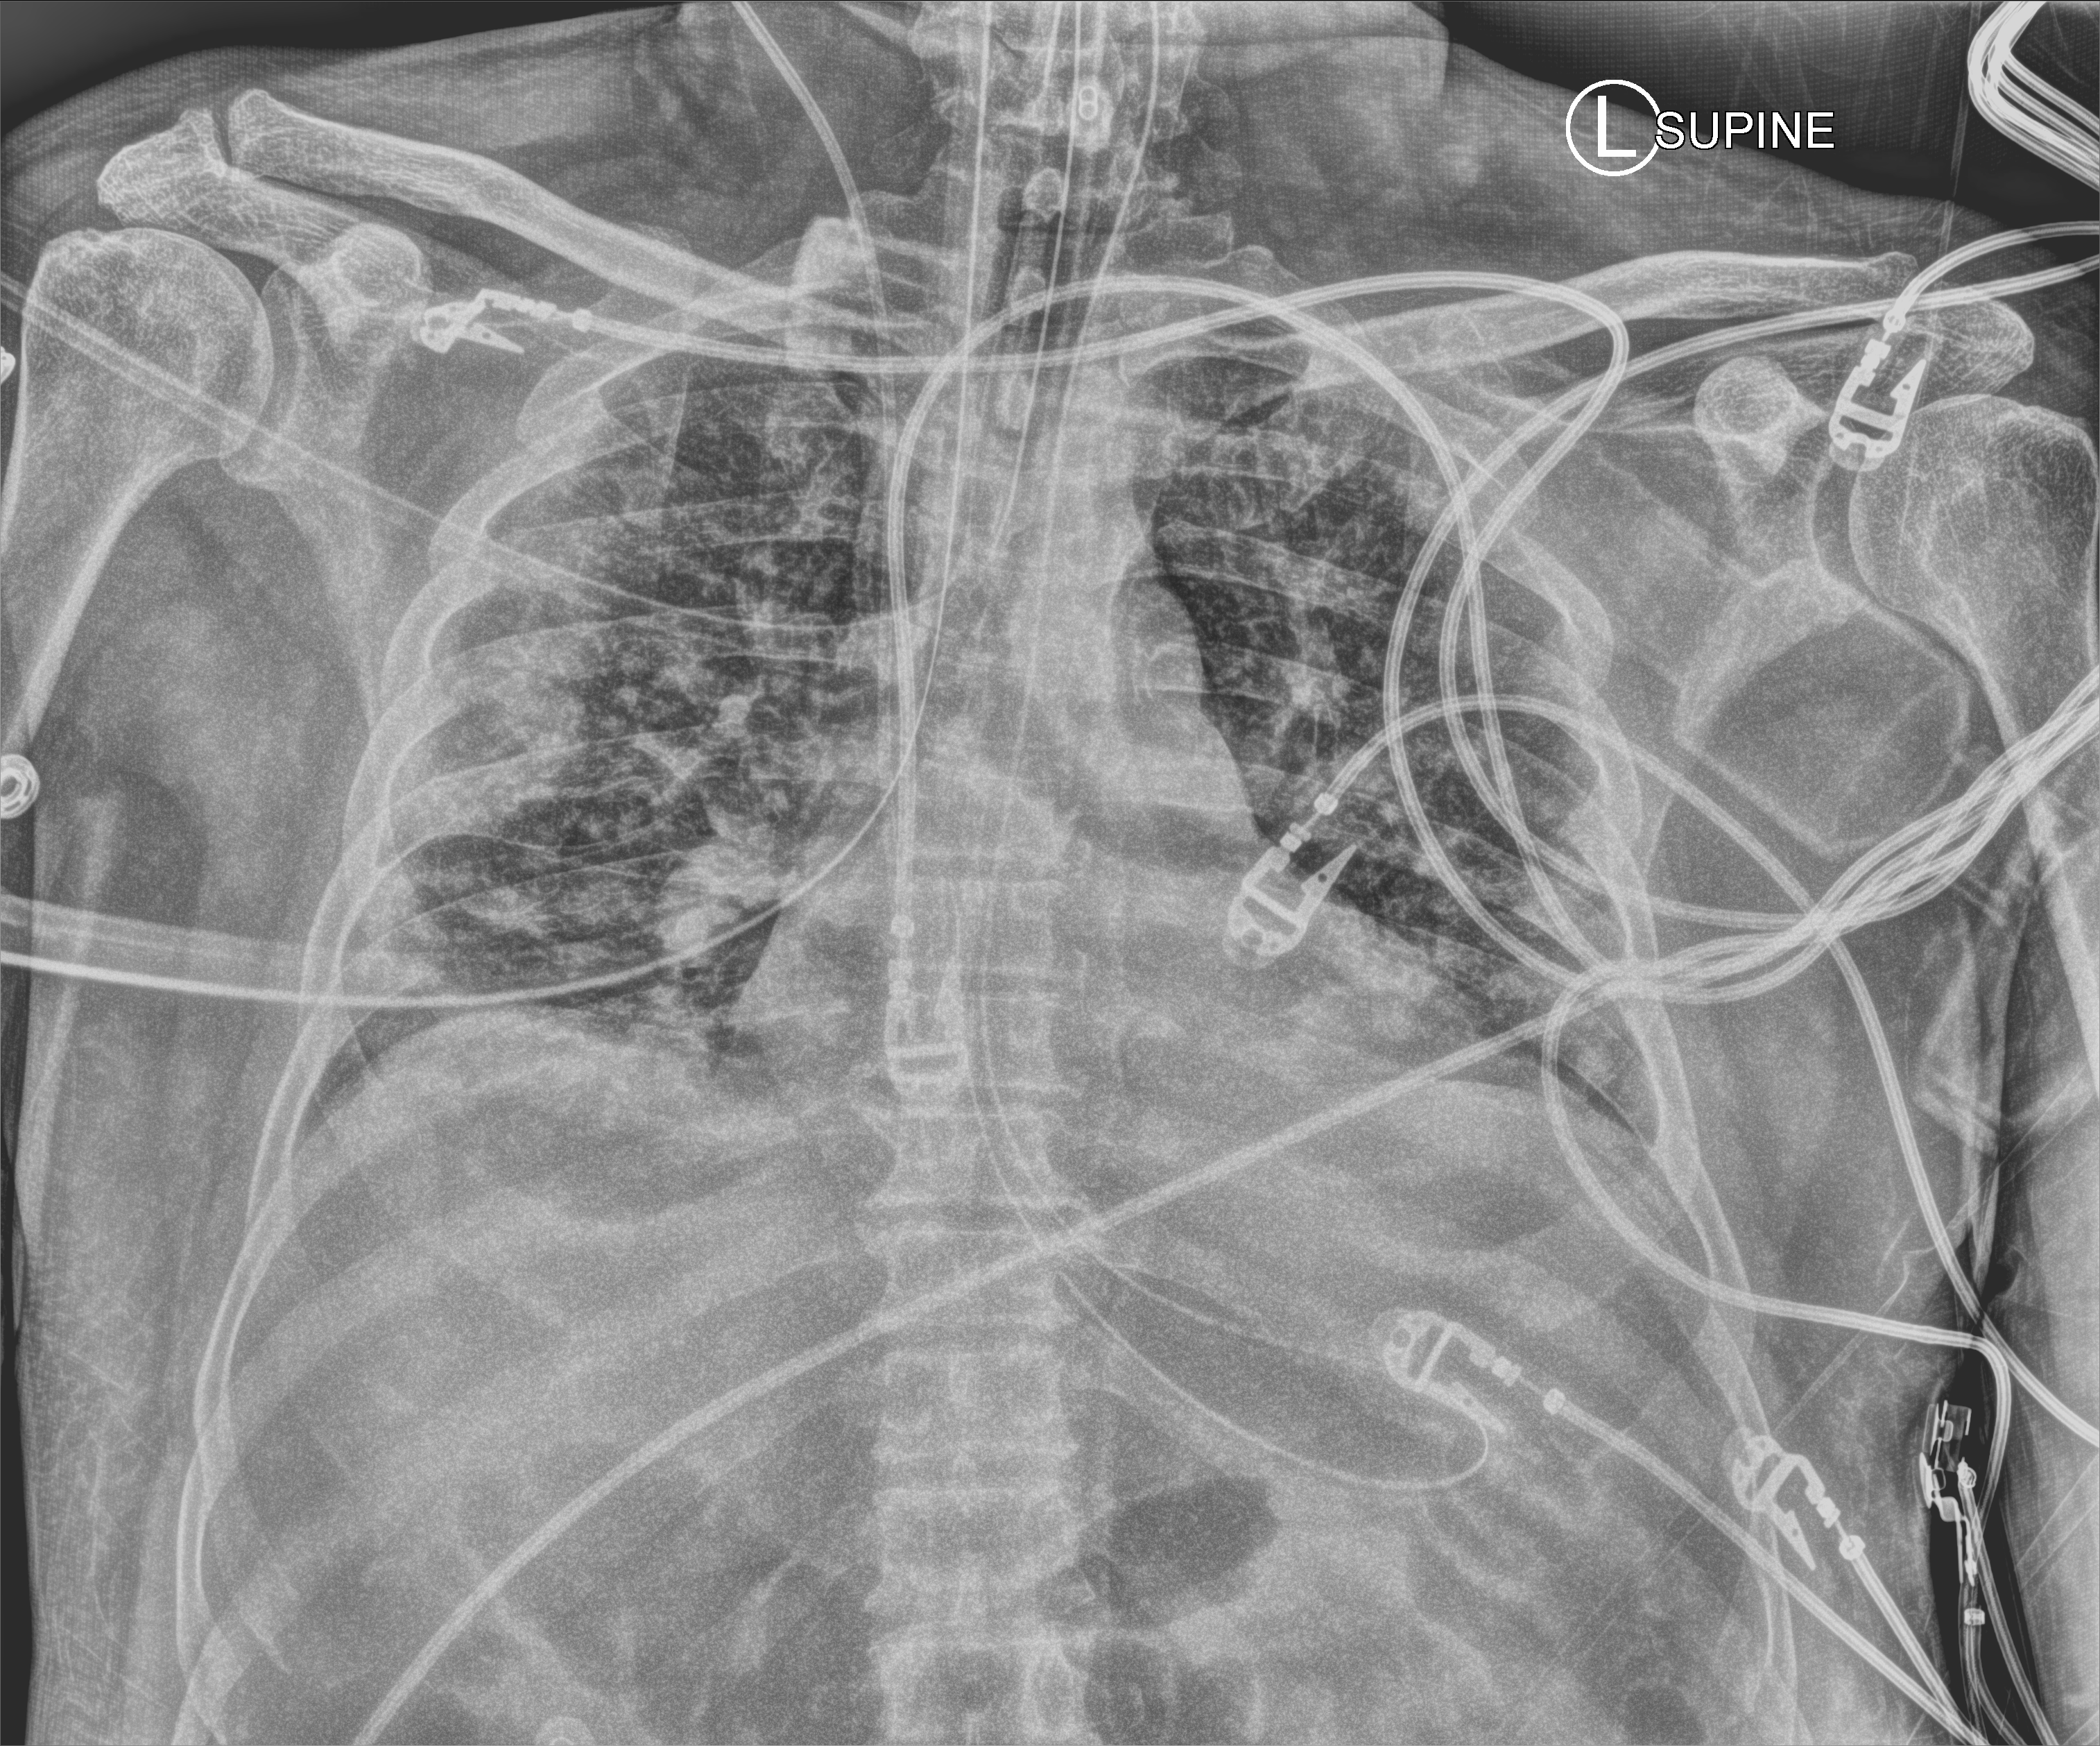
Bedside chest radiograph (computed radiography). Male patient hospitalised with COVID-19, age 18–59 years.
From the hospital-stay record, not from the radiograph (when in the stay this image was taken is not recorded):
- other chronic lung disease (admission record): no